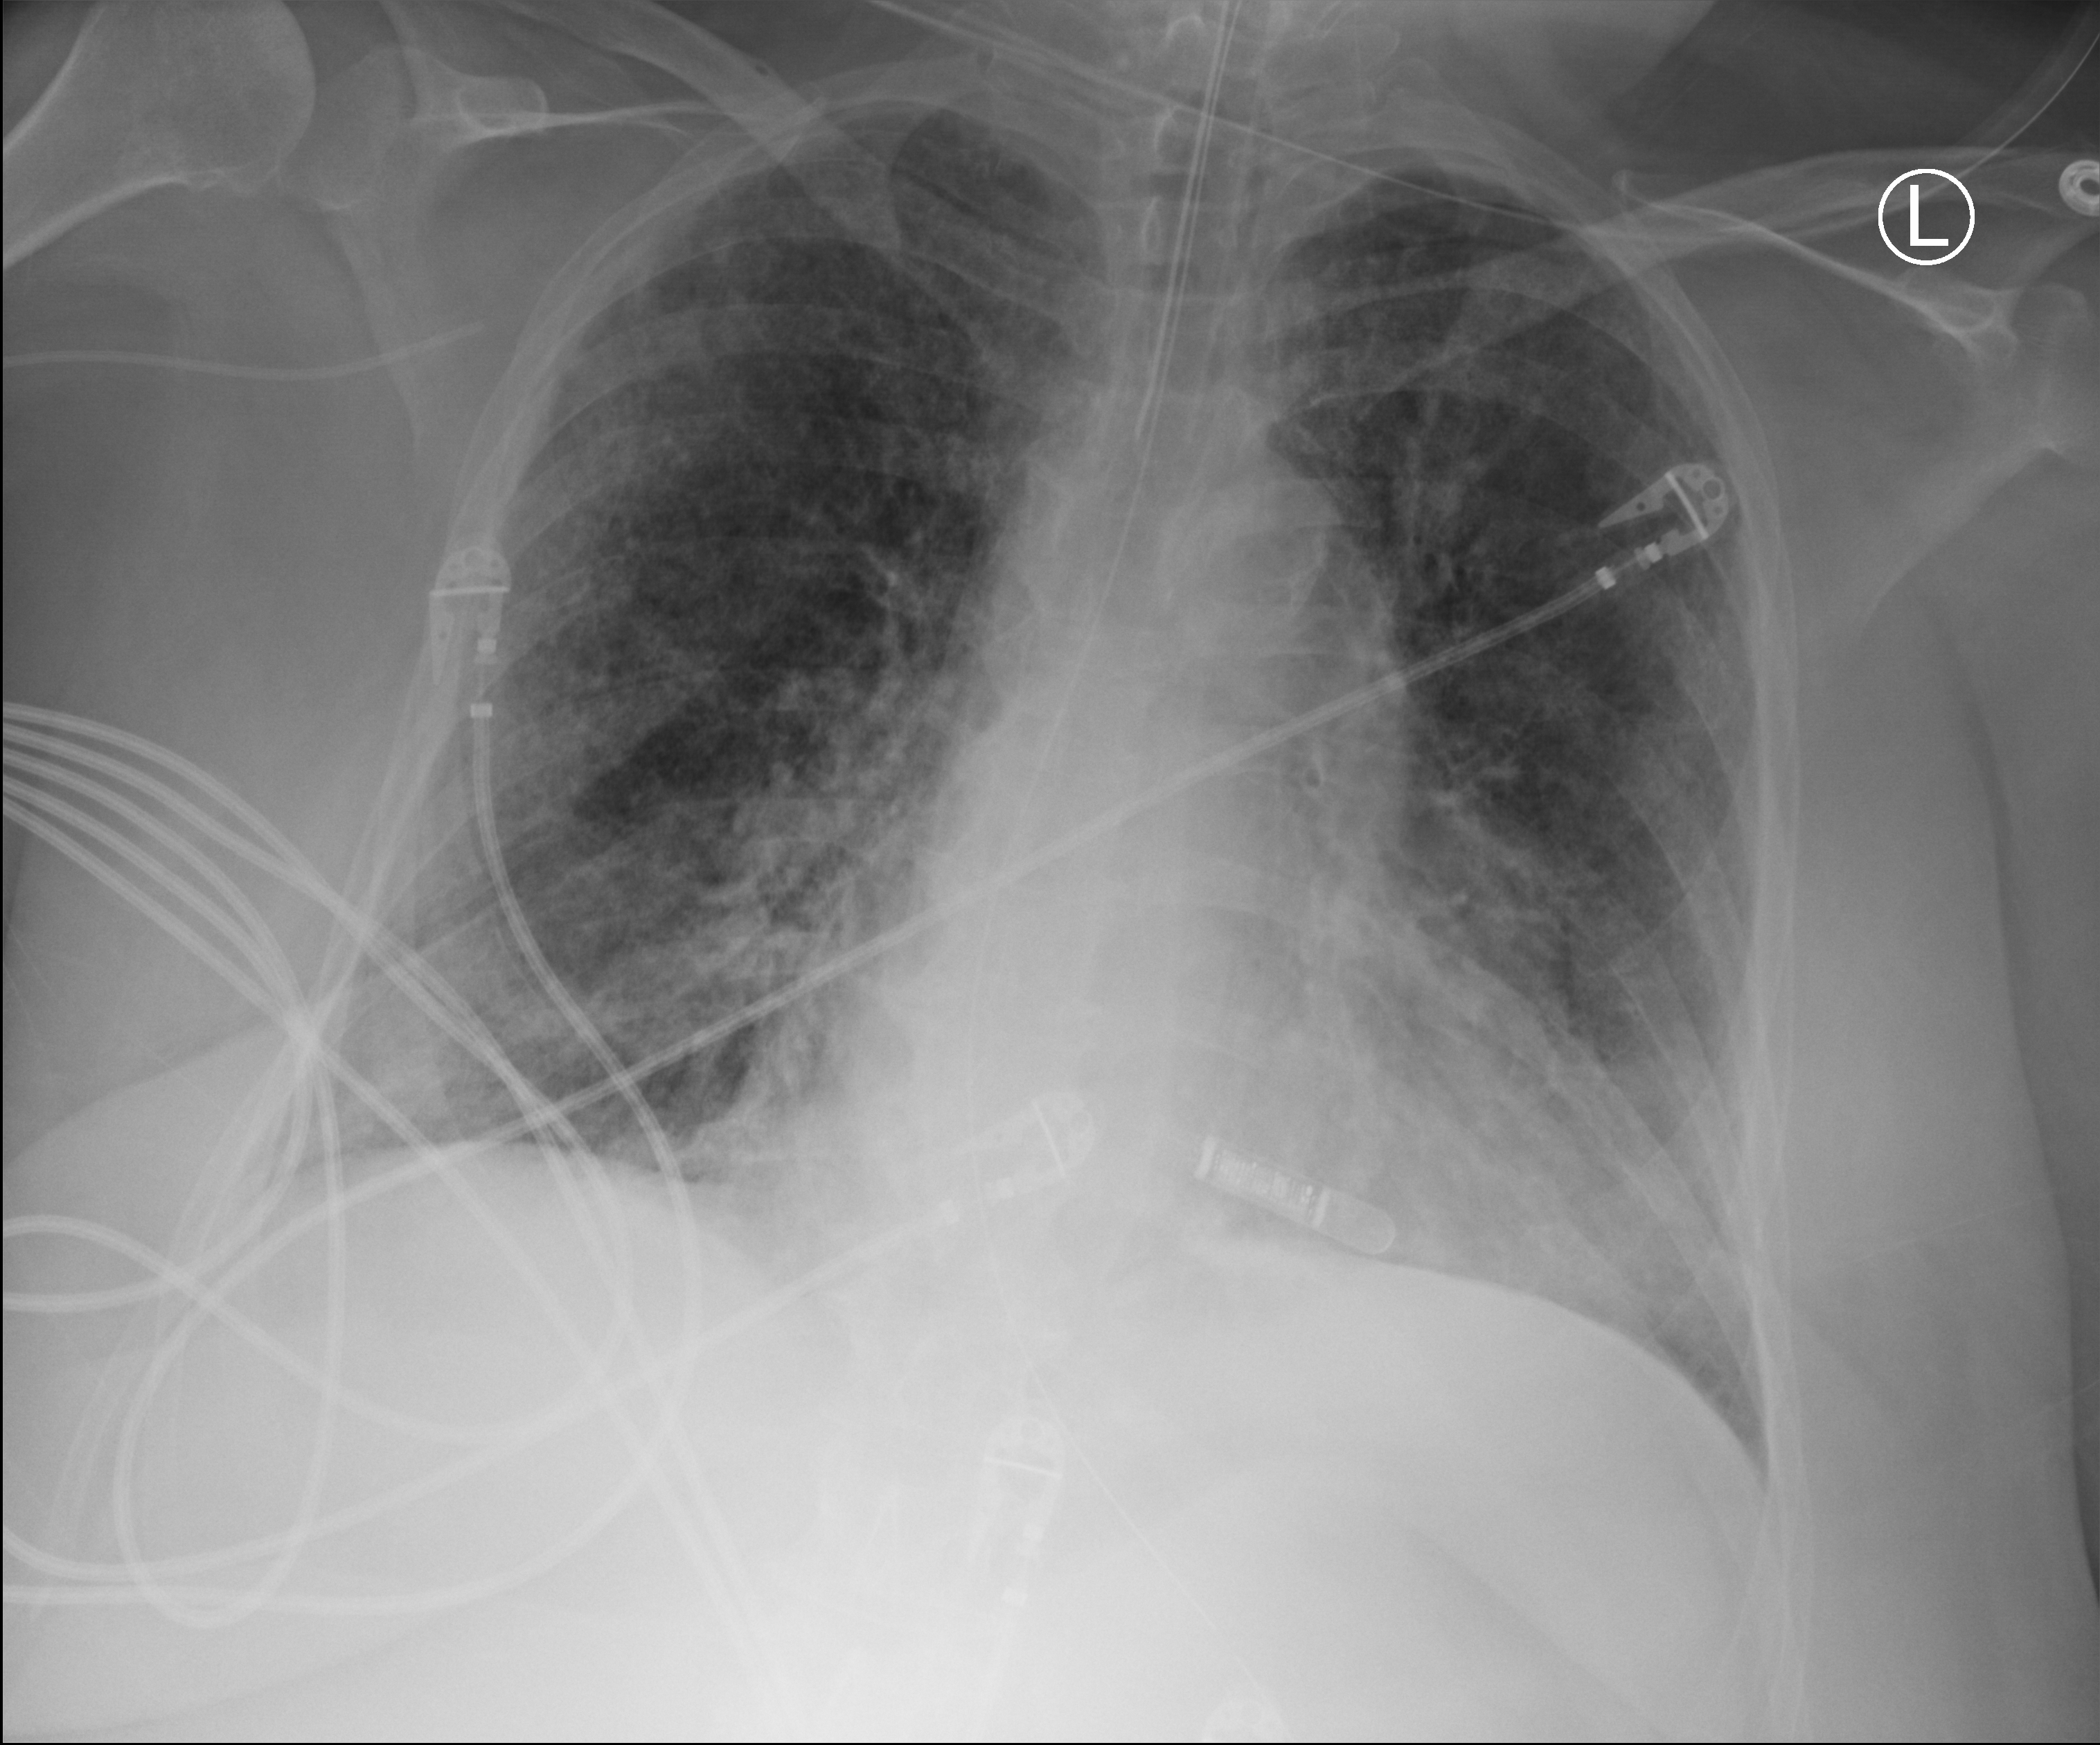
Portable chest radiograph. Female patient hospitalised with COVID-19, age 60–74 years.
From the hospital-stay record, not from the radiograph (when in the stay this image was taken is not recorded): mechanically ventilated during this hospital stay: yes; other chronic lung disease (admission record): yes.